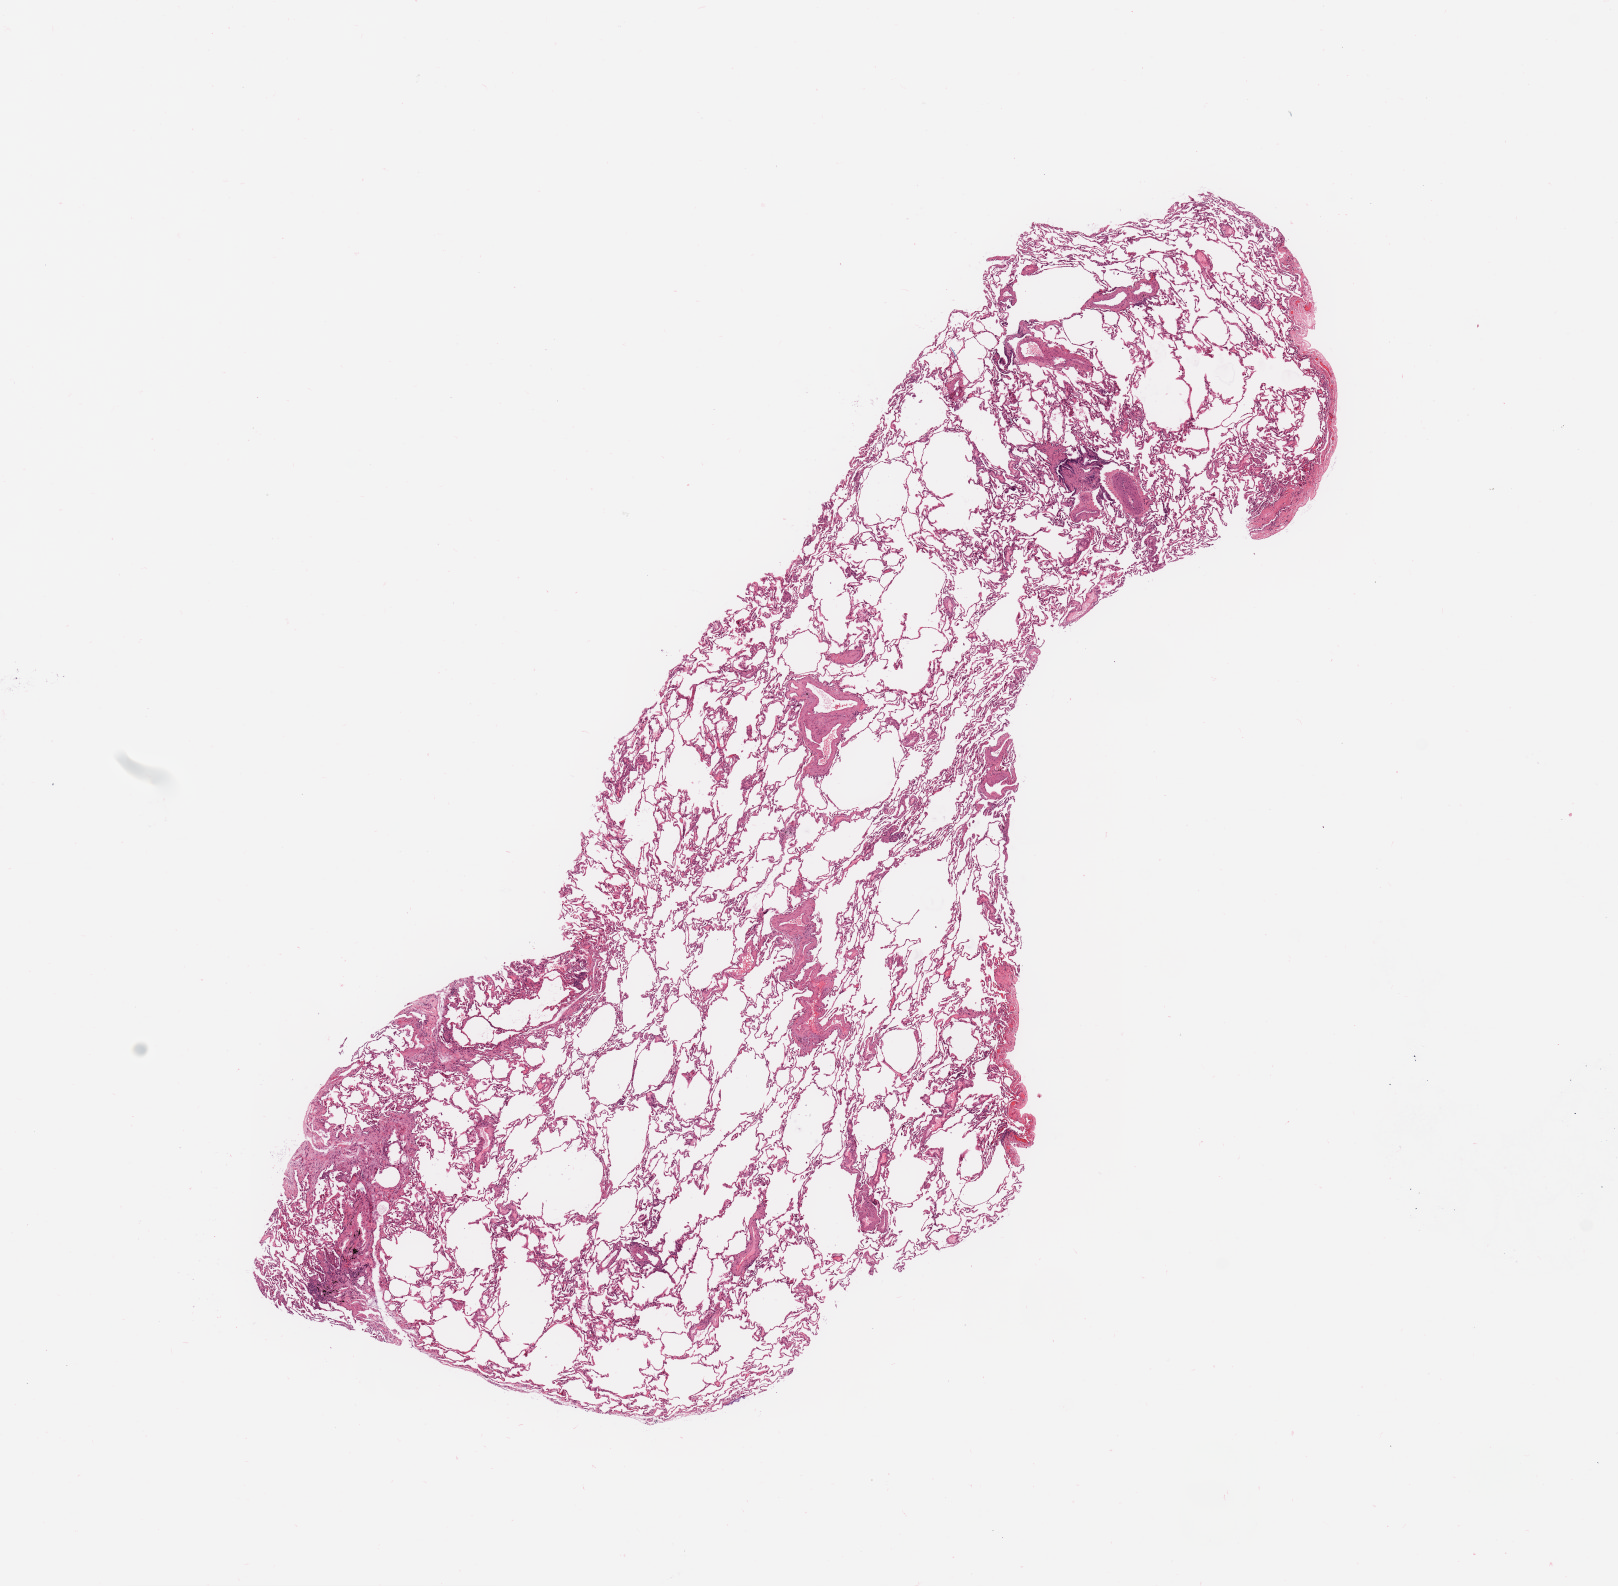
Whole-slide histology image, H&E-stained — shown as a low-resolution overview of the whole scanned area (about 12.8 x 12.5 mm, acquisition: 20x scan), normal (non-tumour) tissue sample, sampled site: lung. Patient: female, age 70 years.
This section: normal (non-tumour) tissue from the same patient. Patient diagnosis: Adenocarcinoma, NOS.